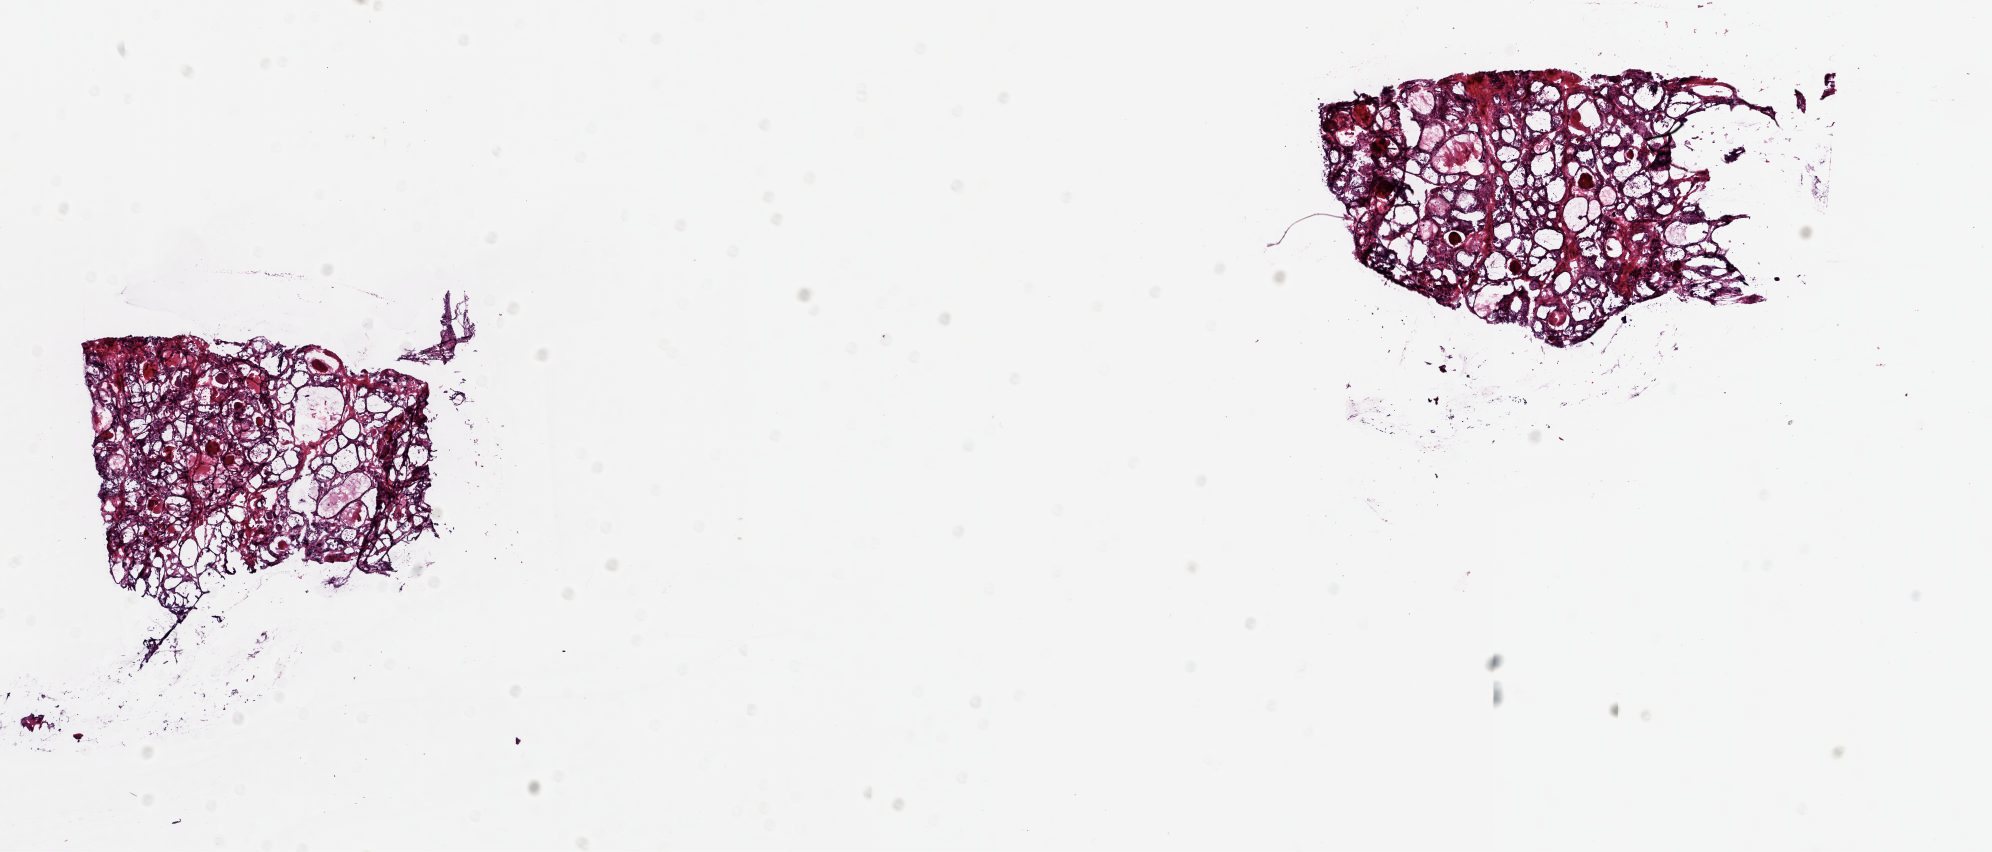
Digitized H&E-stained tissue section (whole slide), a low-resolution overview of the entire scanned area, about 15.8 x 6.8 mm (slide scanned at 20x), frozen section from the top of the tissue portion, solid tissue normal (non-tumour tissue) sample from the thyroid. Female, age 47 years at initial diagnosis.
This section: solid tissue normal sample (biorepository sample class). Patient diagnosis: Papillary carcinoma, follicular variant (thyroid gland).